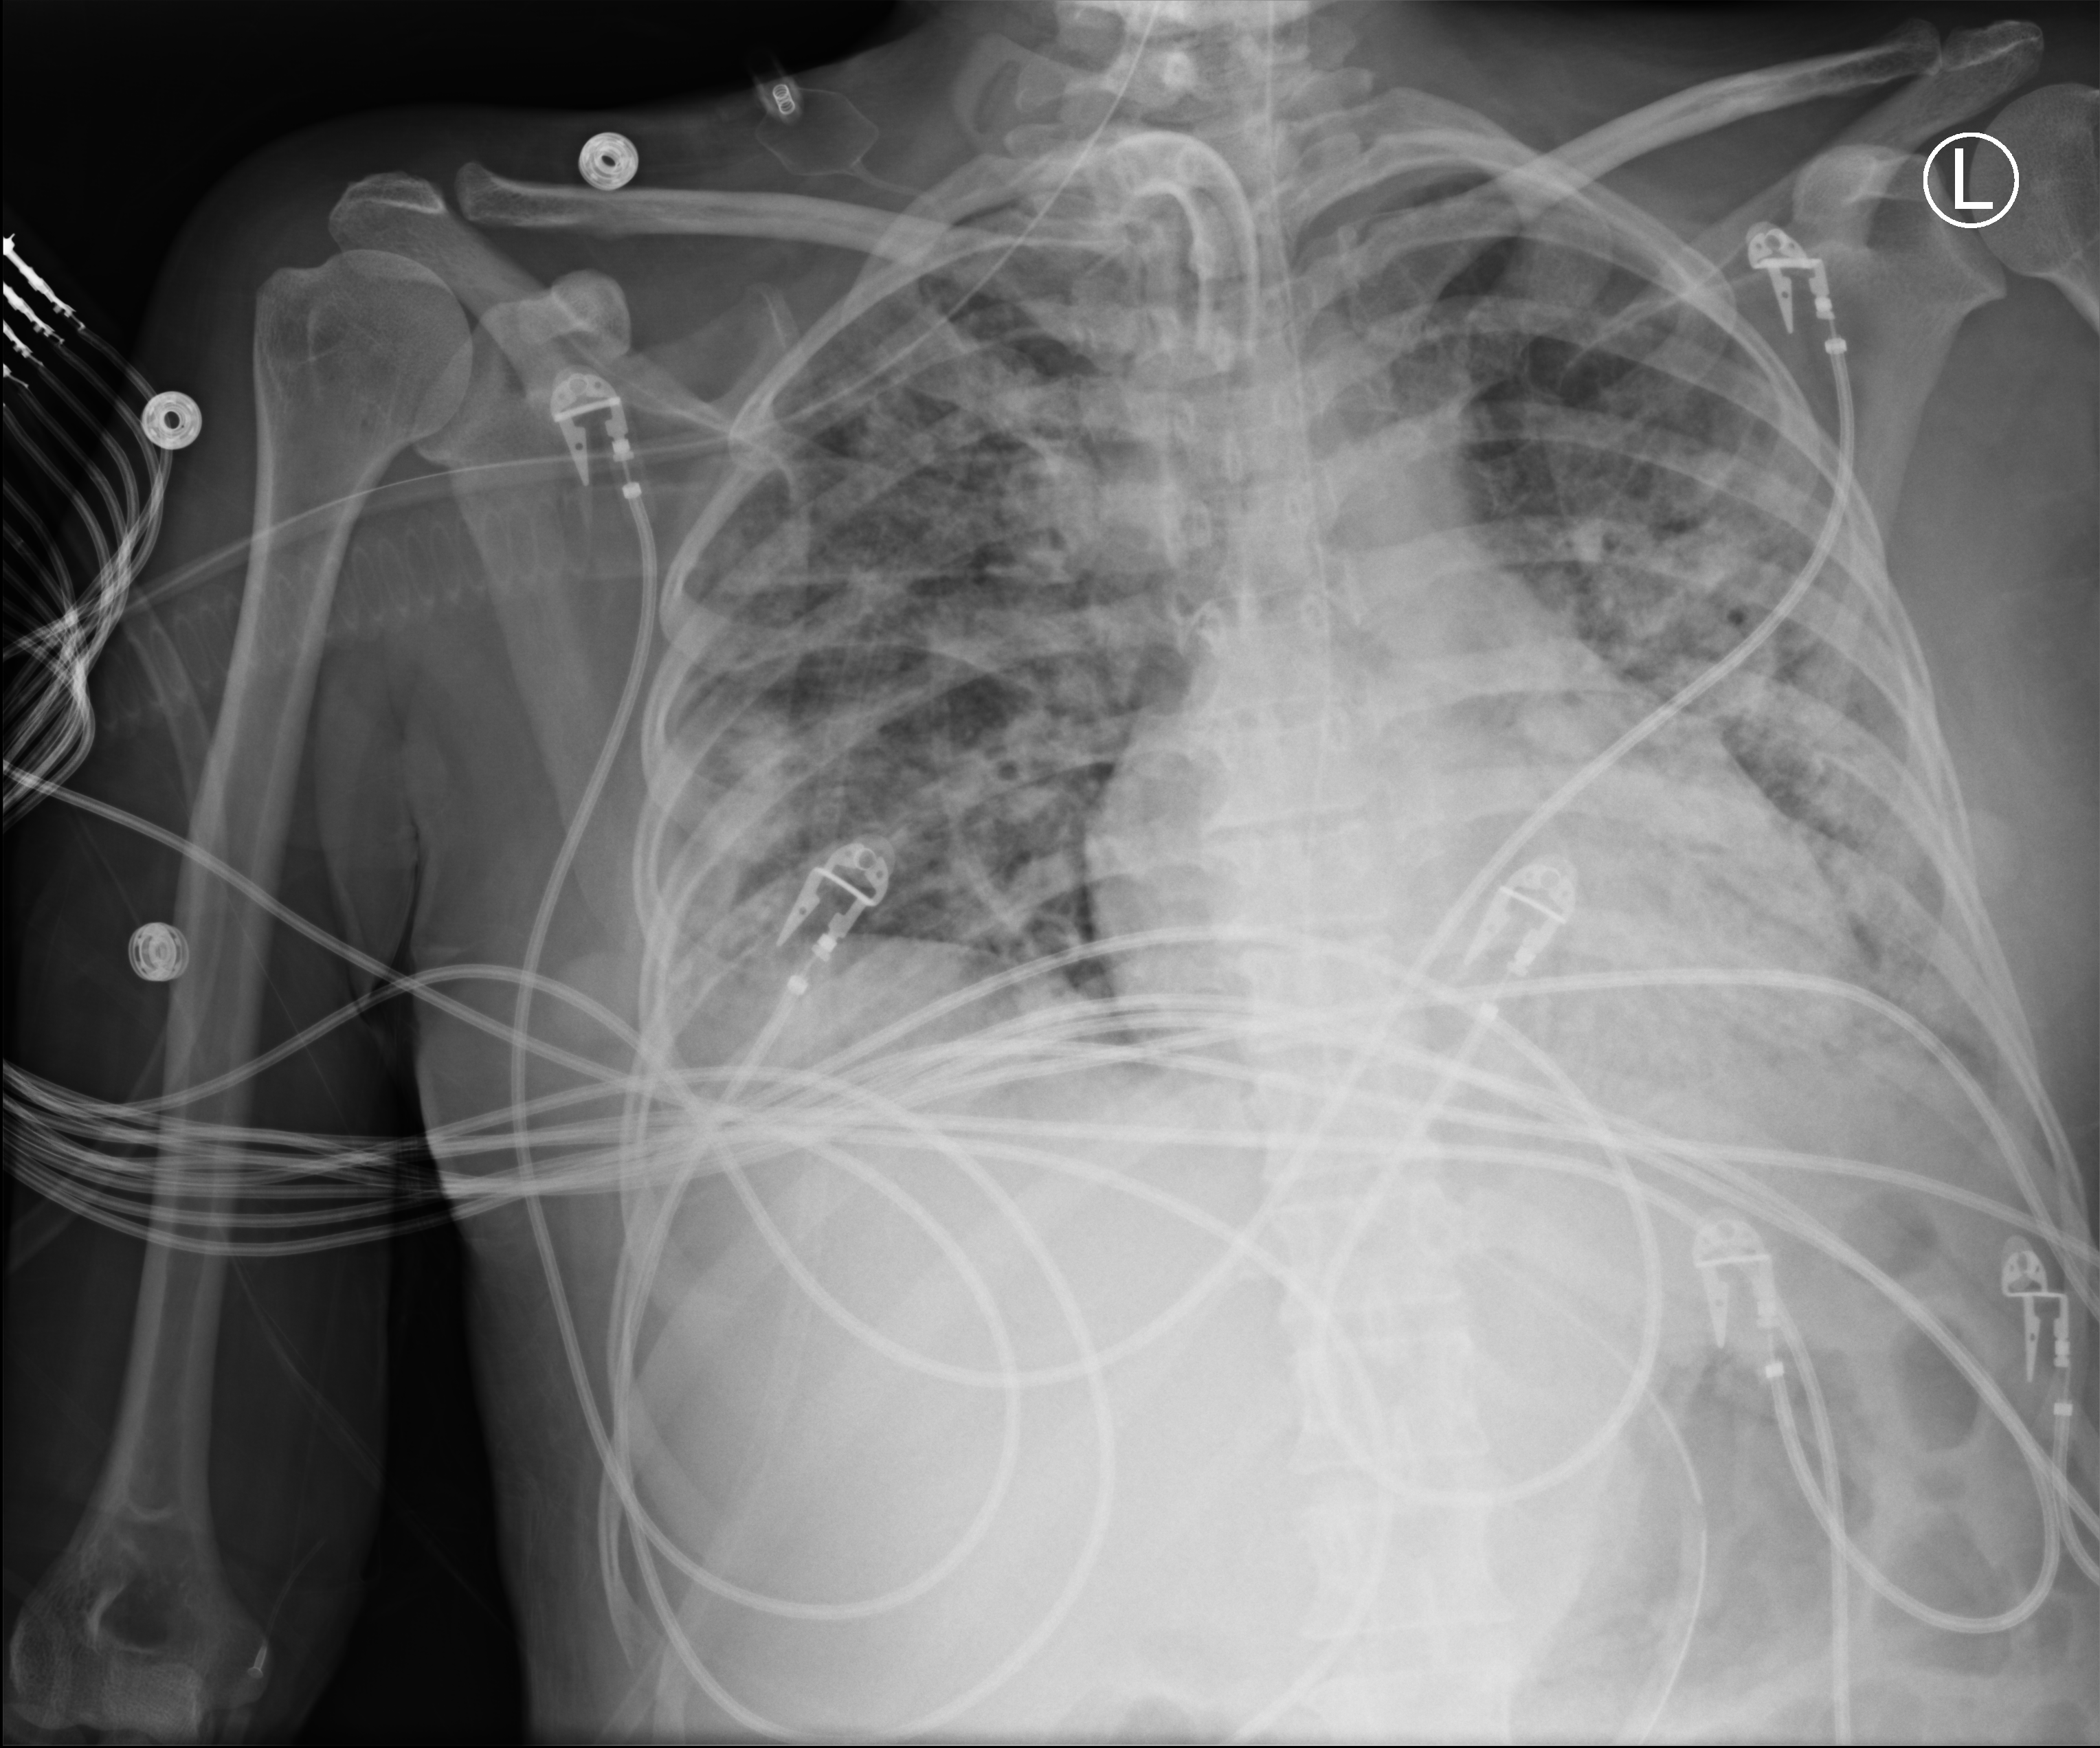
Chest X-ray (portable), anteroposterior (AP) projection. Patient hospitalised with COVID-19; female, aged 18–59 years.
From the hospital-stay record, not from the radiograph (when in the stay this image was taken is not recorded):
- admitted to intensive care during this hospital stay: yes